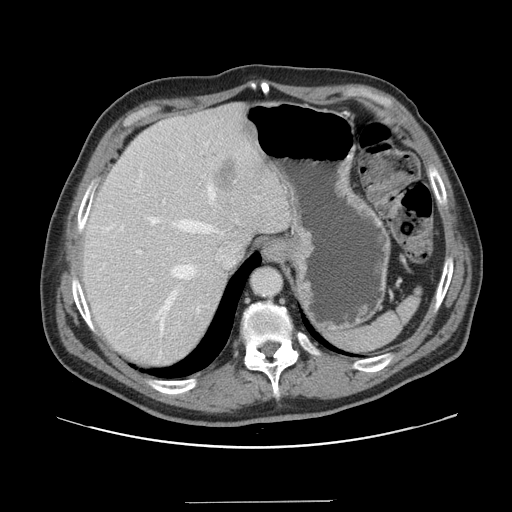
Contrast-enhanced abdominal CT, one axial slice; slice 121 of 151 in the series (ordered by position); soft-tissue window (W 400 / L 40 HU); 2.5 mm slice thickness; 512 × 512 image matrix, field of view 399 × 399 mm. Male patient, age 63 years. Case-level facts recorded for this patient, not image findings: diagnosis: colorectal cancer liver metastases, imaged before liver resection; multiple liver metastases: no; largest metastasis: 2.1 cm; disease in both lobes: no.
Outlined on this slice (manually delineated by an expert):
- hepatic veins: box from (x=147, y=184) to (x=217, y=333) px
- liver: (x=82, y=106)–(x=291, y=368)
- planned liver remnant (the part of the liver to remain after resection): (x=82, y=117)–(x=255, y=367)
- portal vein (with intrahepatic branches): (x=136, y=202)–(x=165, y=280)
- liver metastasis: (x=214, y=158)–(x=238, y=192)